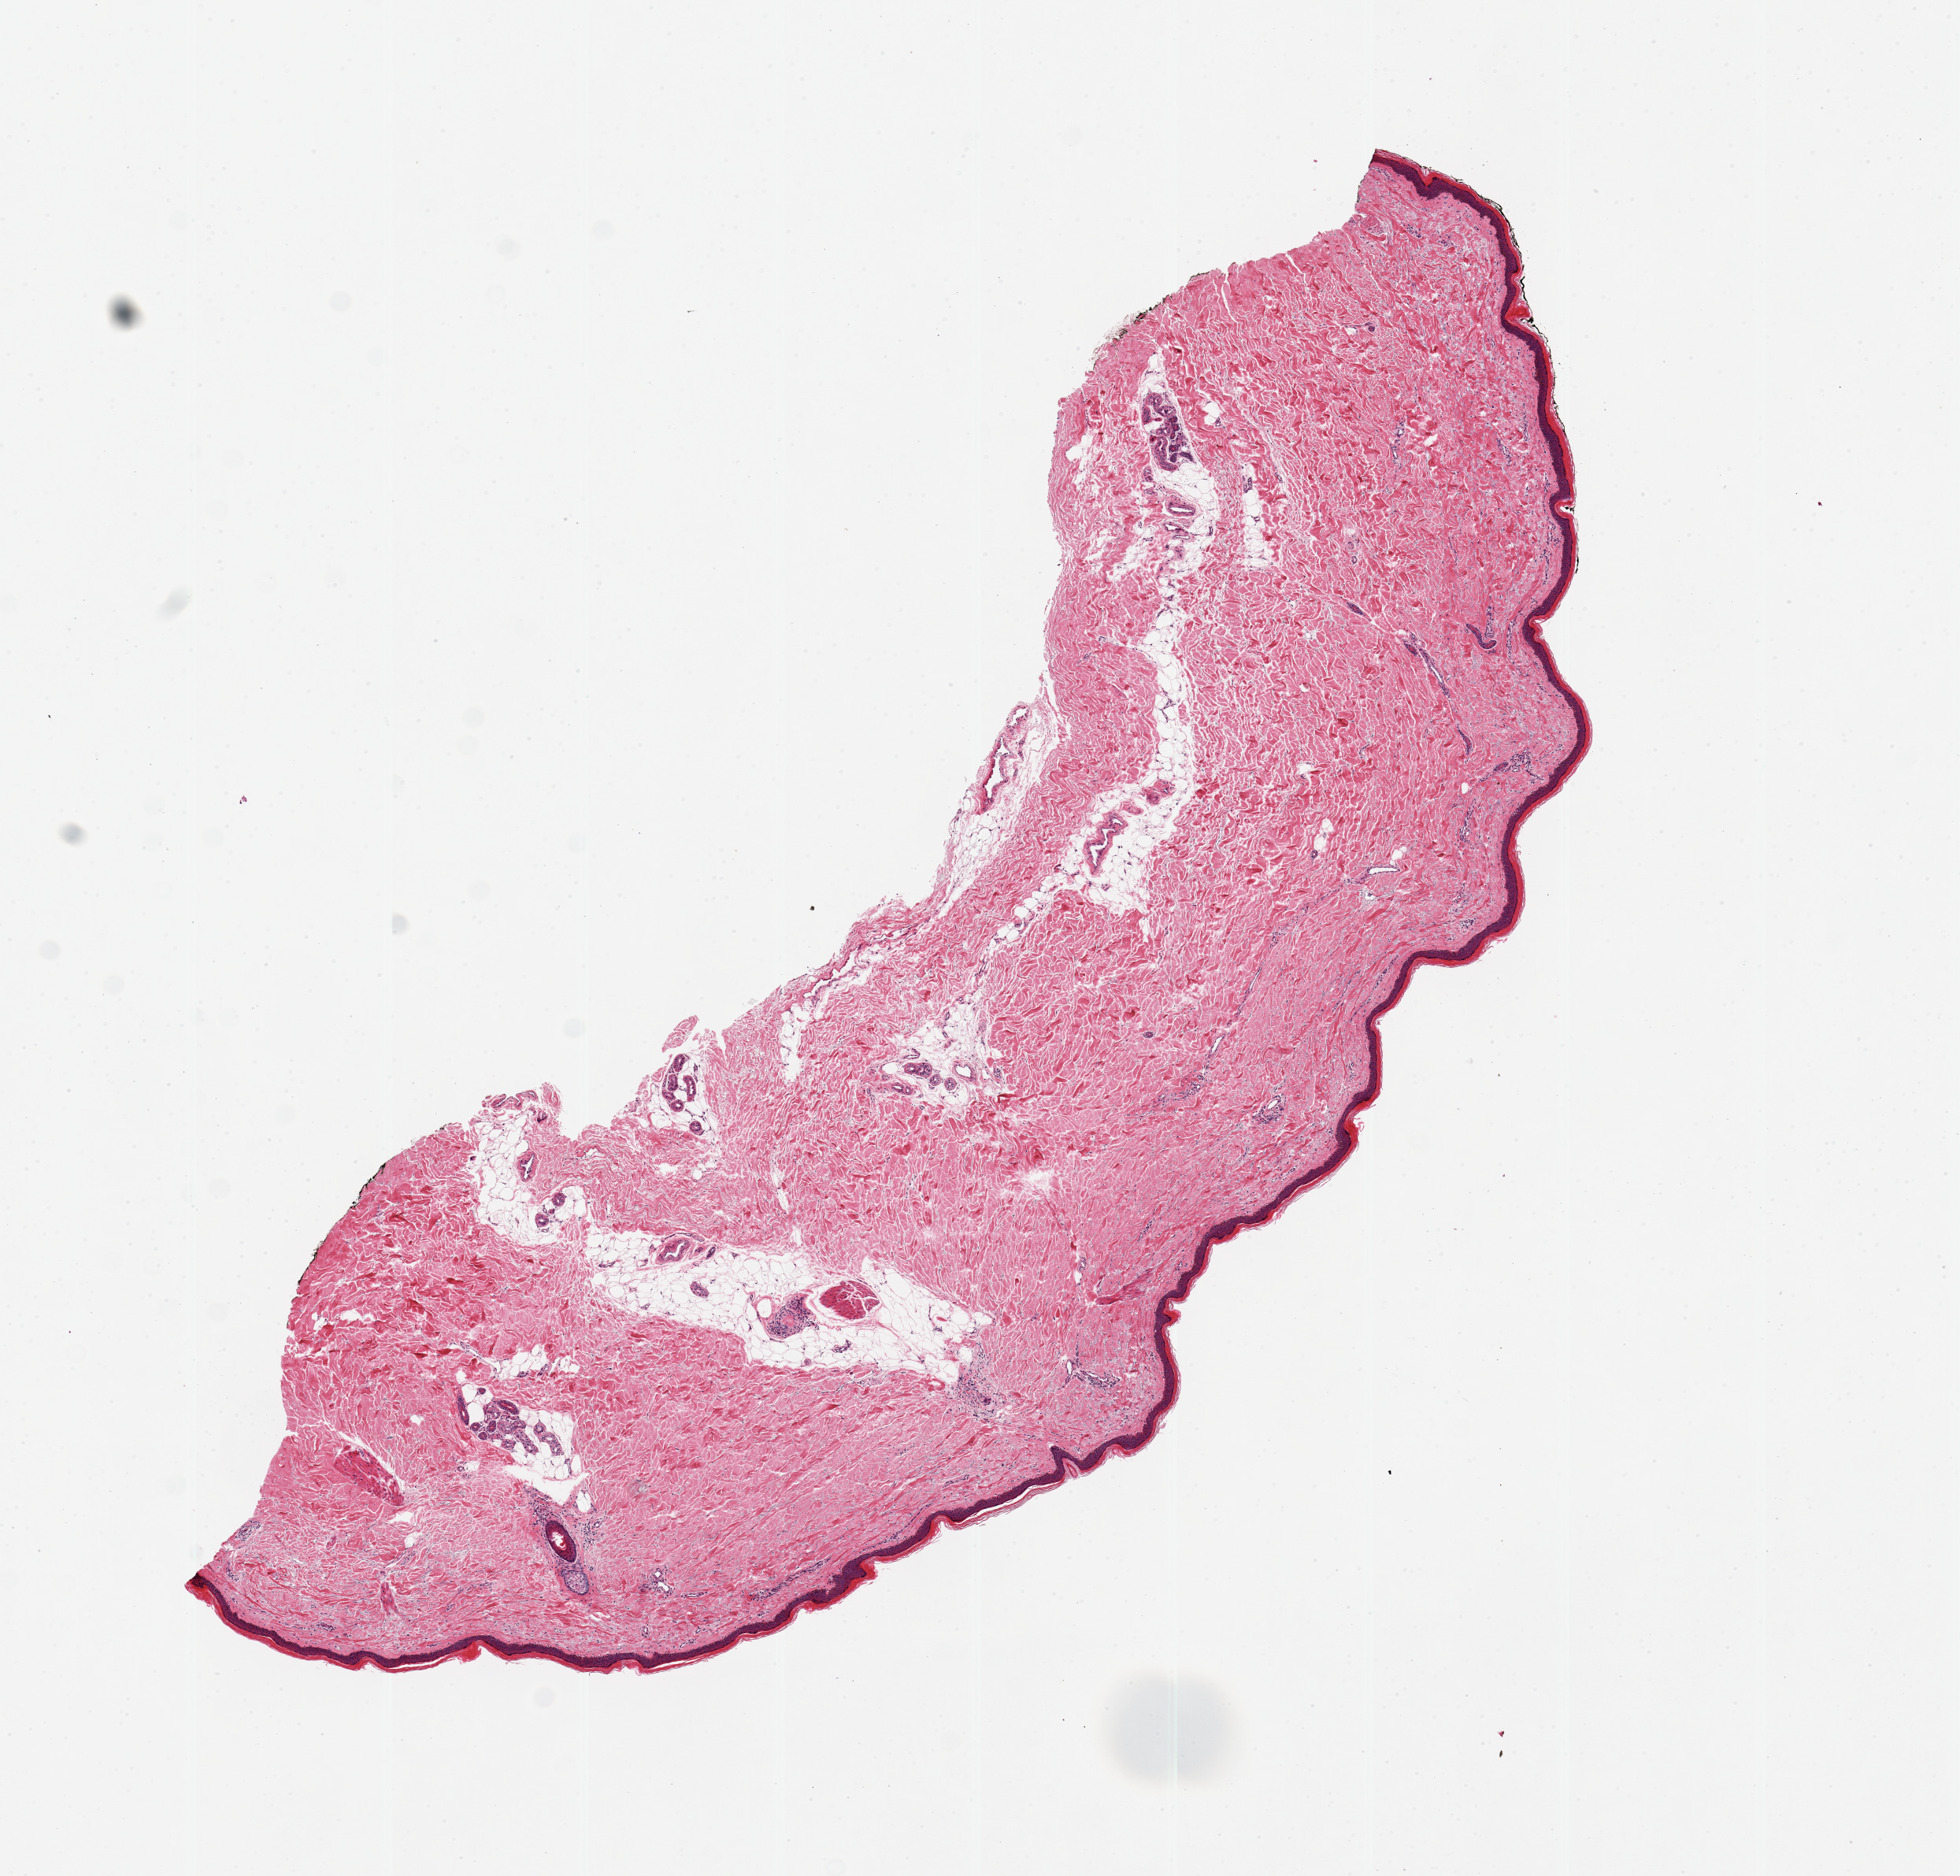
Whole-slide image, haematoxylin and eosin stain — shown as a low-resolution overview of the whole scanned area (about 9.8 x 9.4 mm, from a 20x scan); PAXgene-fixed, paraffin-embedded tissue; target tissue: skin of lower leg; tissue donor sample. Donor sex: female.
Reviewer comment on this tissue sample: 1 piece. 10x4mm; well trimmed subcutaneous fat; about 10% internal adipose.